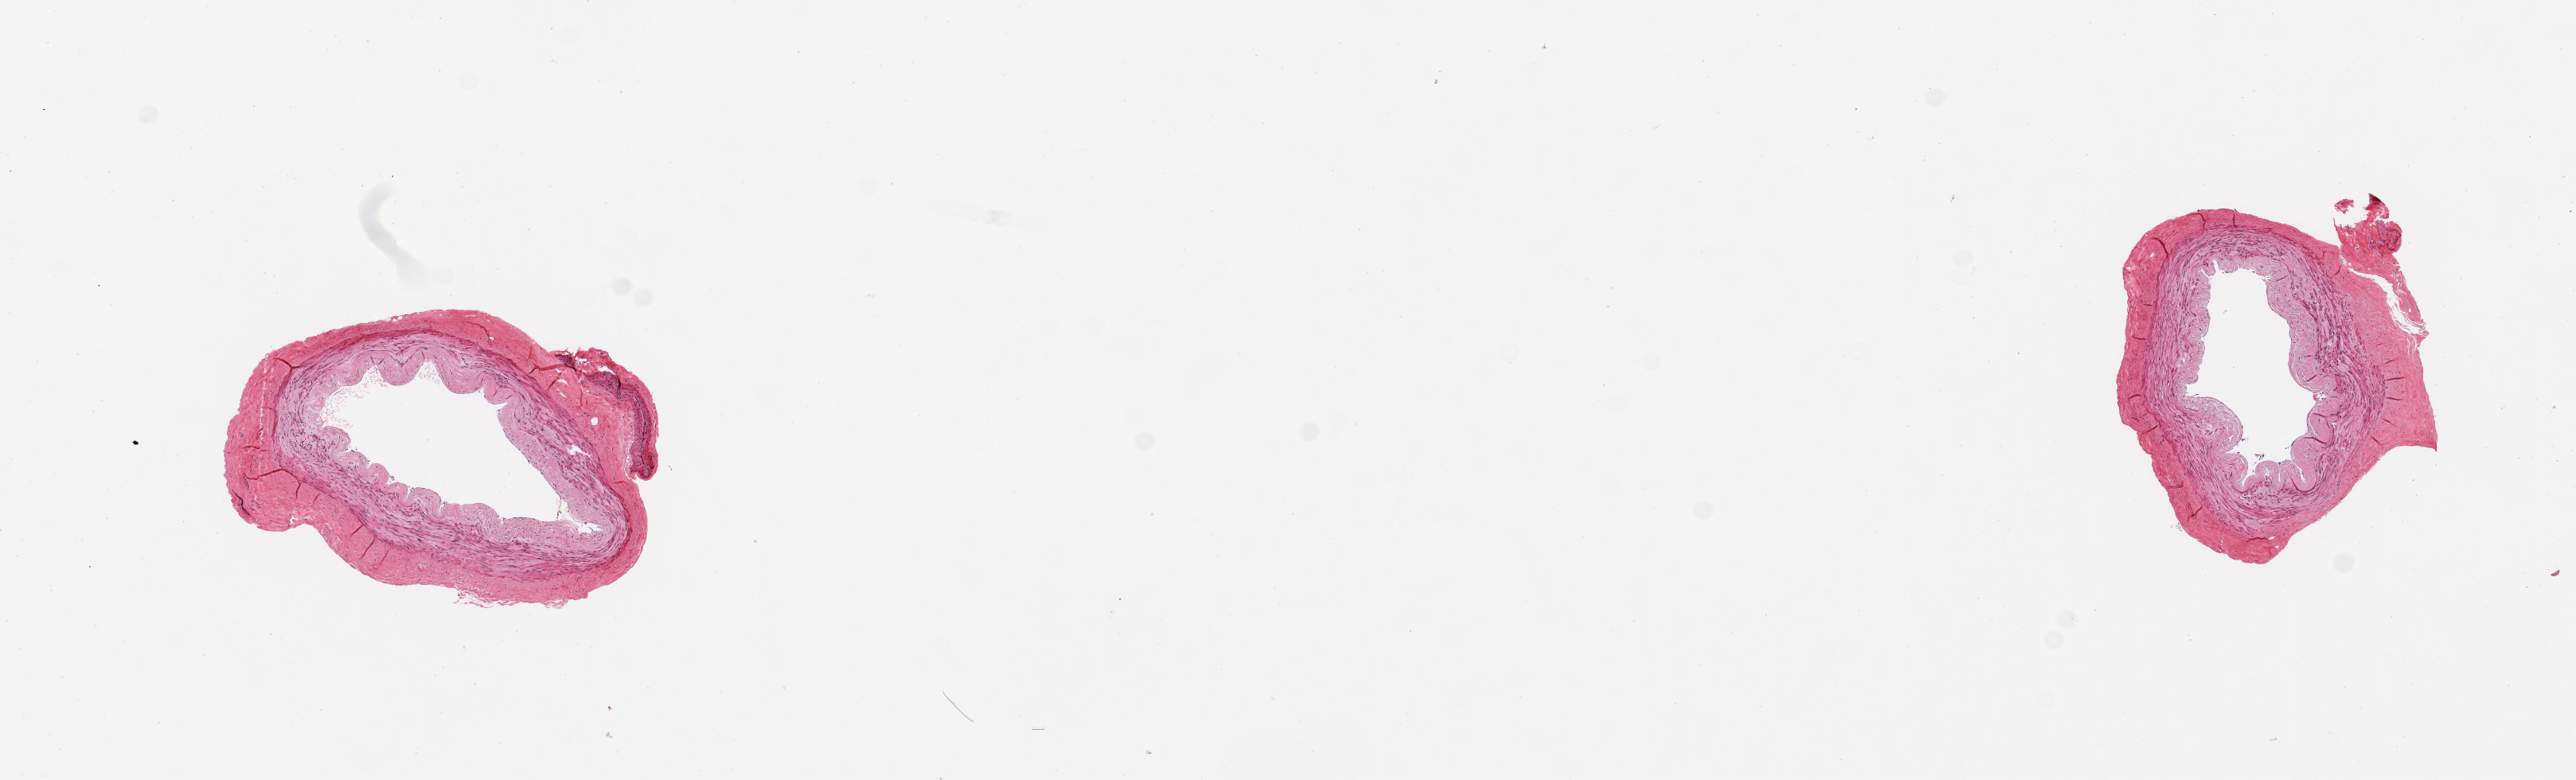
Whole-slide image, hematoxylin and eosin (H&E) stain — whole scanned area (about 12.8 x 3.9 mm) shown as a low-resolution overview; PAXgene-fixed paraffin-embedded (PFPE) section; section of tibial artery (target tissue); donor tissue sample. Female donor.
Pathologist's review note for this sample: 2 pieces, no significant atherosis or adherent fat.